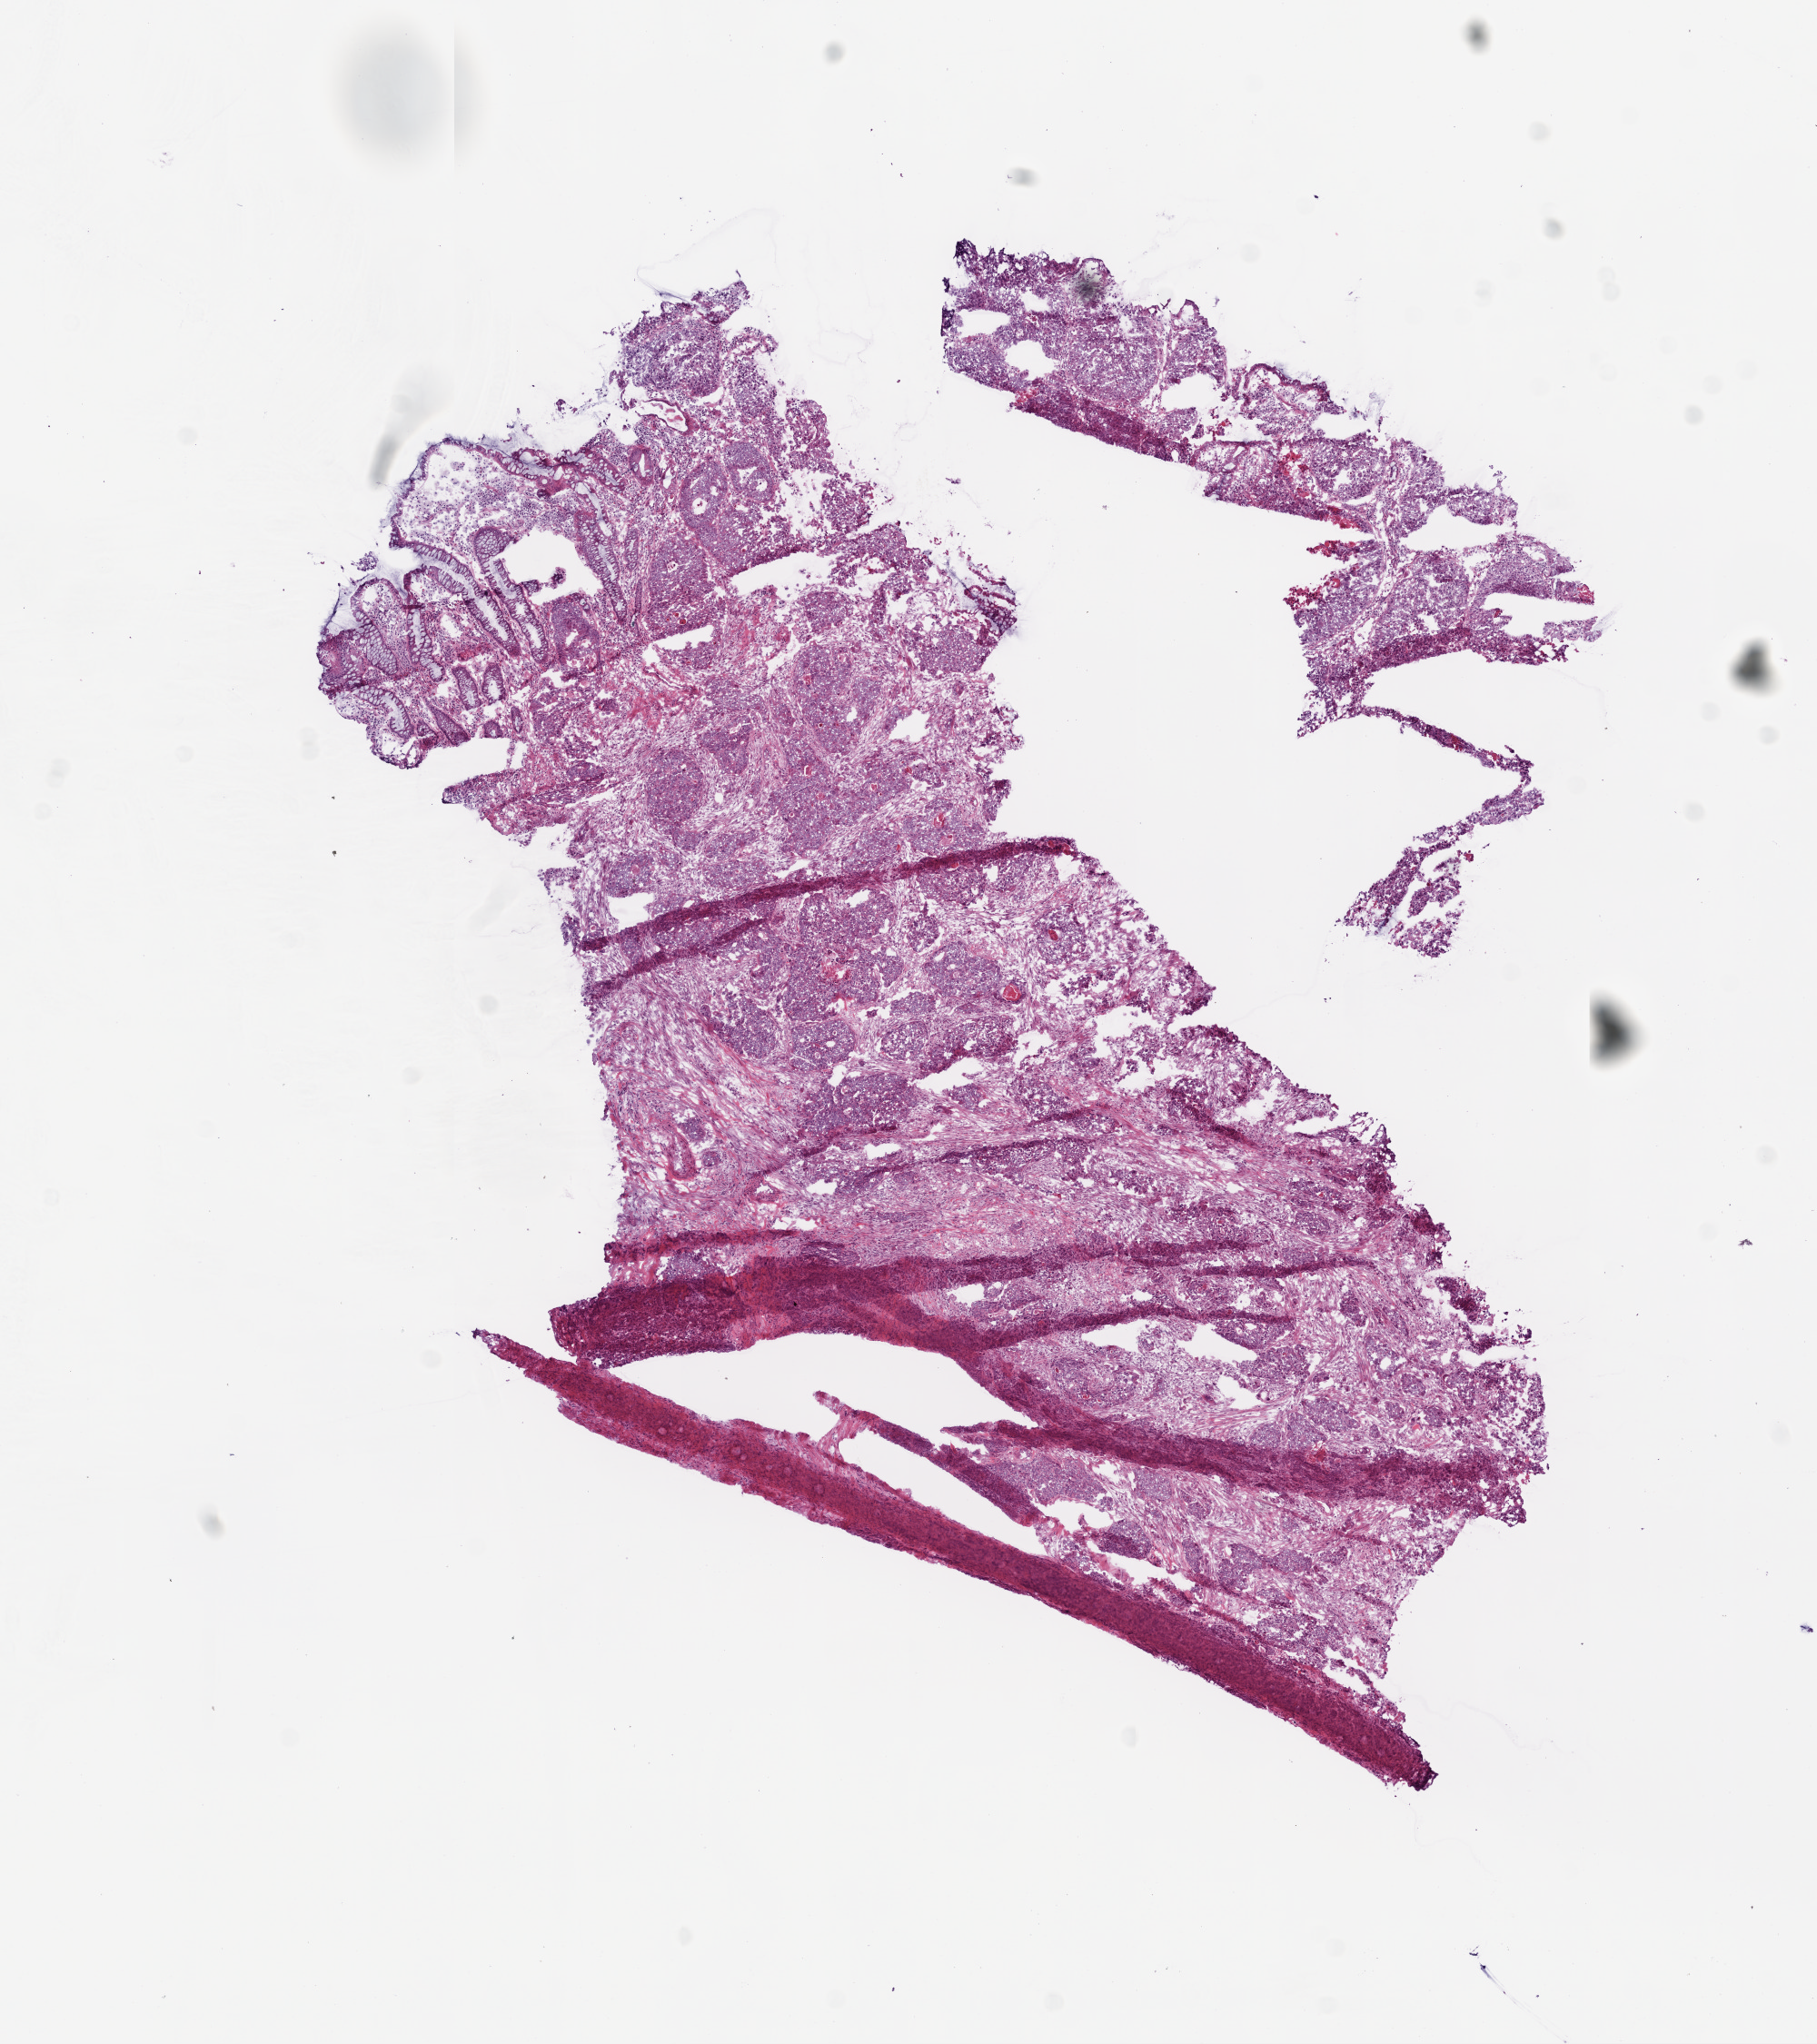
Digitized H&E tissue section (whole slide) — low-resolution overview of the scanned area, about 8.0 x 9.0 mm (from a 20x scan), frozen section, colon, primary tumour sample. Patient: male, age at initial diagnosis 73 years. Composition of this section per pathologist review: tumour cells 85%, tumour nuclei 85%, normal cells 0%, stromal cells 10%, necrosis 5%.
• AJCC pathologic stage: IV (6th edition)
• diagnosis: Adenocarcinoma, NOS (sigmoid colon)
• lymph nodes positive (case pathology): 4 of 24 examined